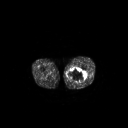
FDG PET of an extremity soft-tissue mass (from a PET/CT study), one axial slice. Slice 235 of 267 in the series (ordered by position). 128 × 128 image matrix, field of view 700 × 700 mm. Patient: male, 44 years. From the clinical record (not read from this slice): histological type: undifferentiated pleomorphic liposarcoma; grade: high; site of the primary tumour: left thigh.
Annotated regions visible in this slice (expert contour drawn on MRI and transferred to this co-registered scan by the dataset authors):
- gross tumour volume including surrounding oedema: bounding box (x1, y1, x2, y2) in pixels: (67, 68, 86, 83)
- gross tumour volume (mass): (67, 68, 86, 83)